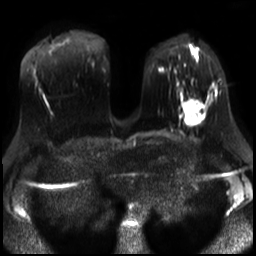
Breast MRI, one axial slice. Position 12 of 30 along the scan axis. Diffusion-weighted series; image 2 of 4 stored at this slice position (different b-values; order by instance number). 3 T. 4 mm slice thickness. 256 × 256 image matrix, field of view 320 × 320 mm. Female patient.
Structures marked on this image (outlined manually by an expert reader):
- tumour on diffusion-weighted imaging: bounding box <183,99,200,121> (left, top, right, bottom; pixels)